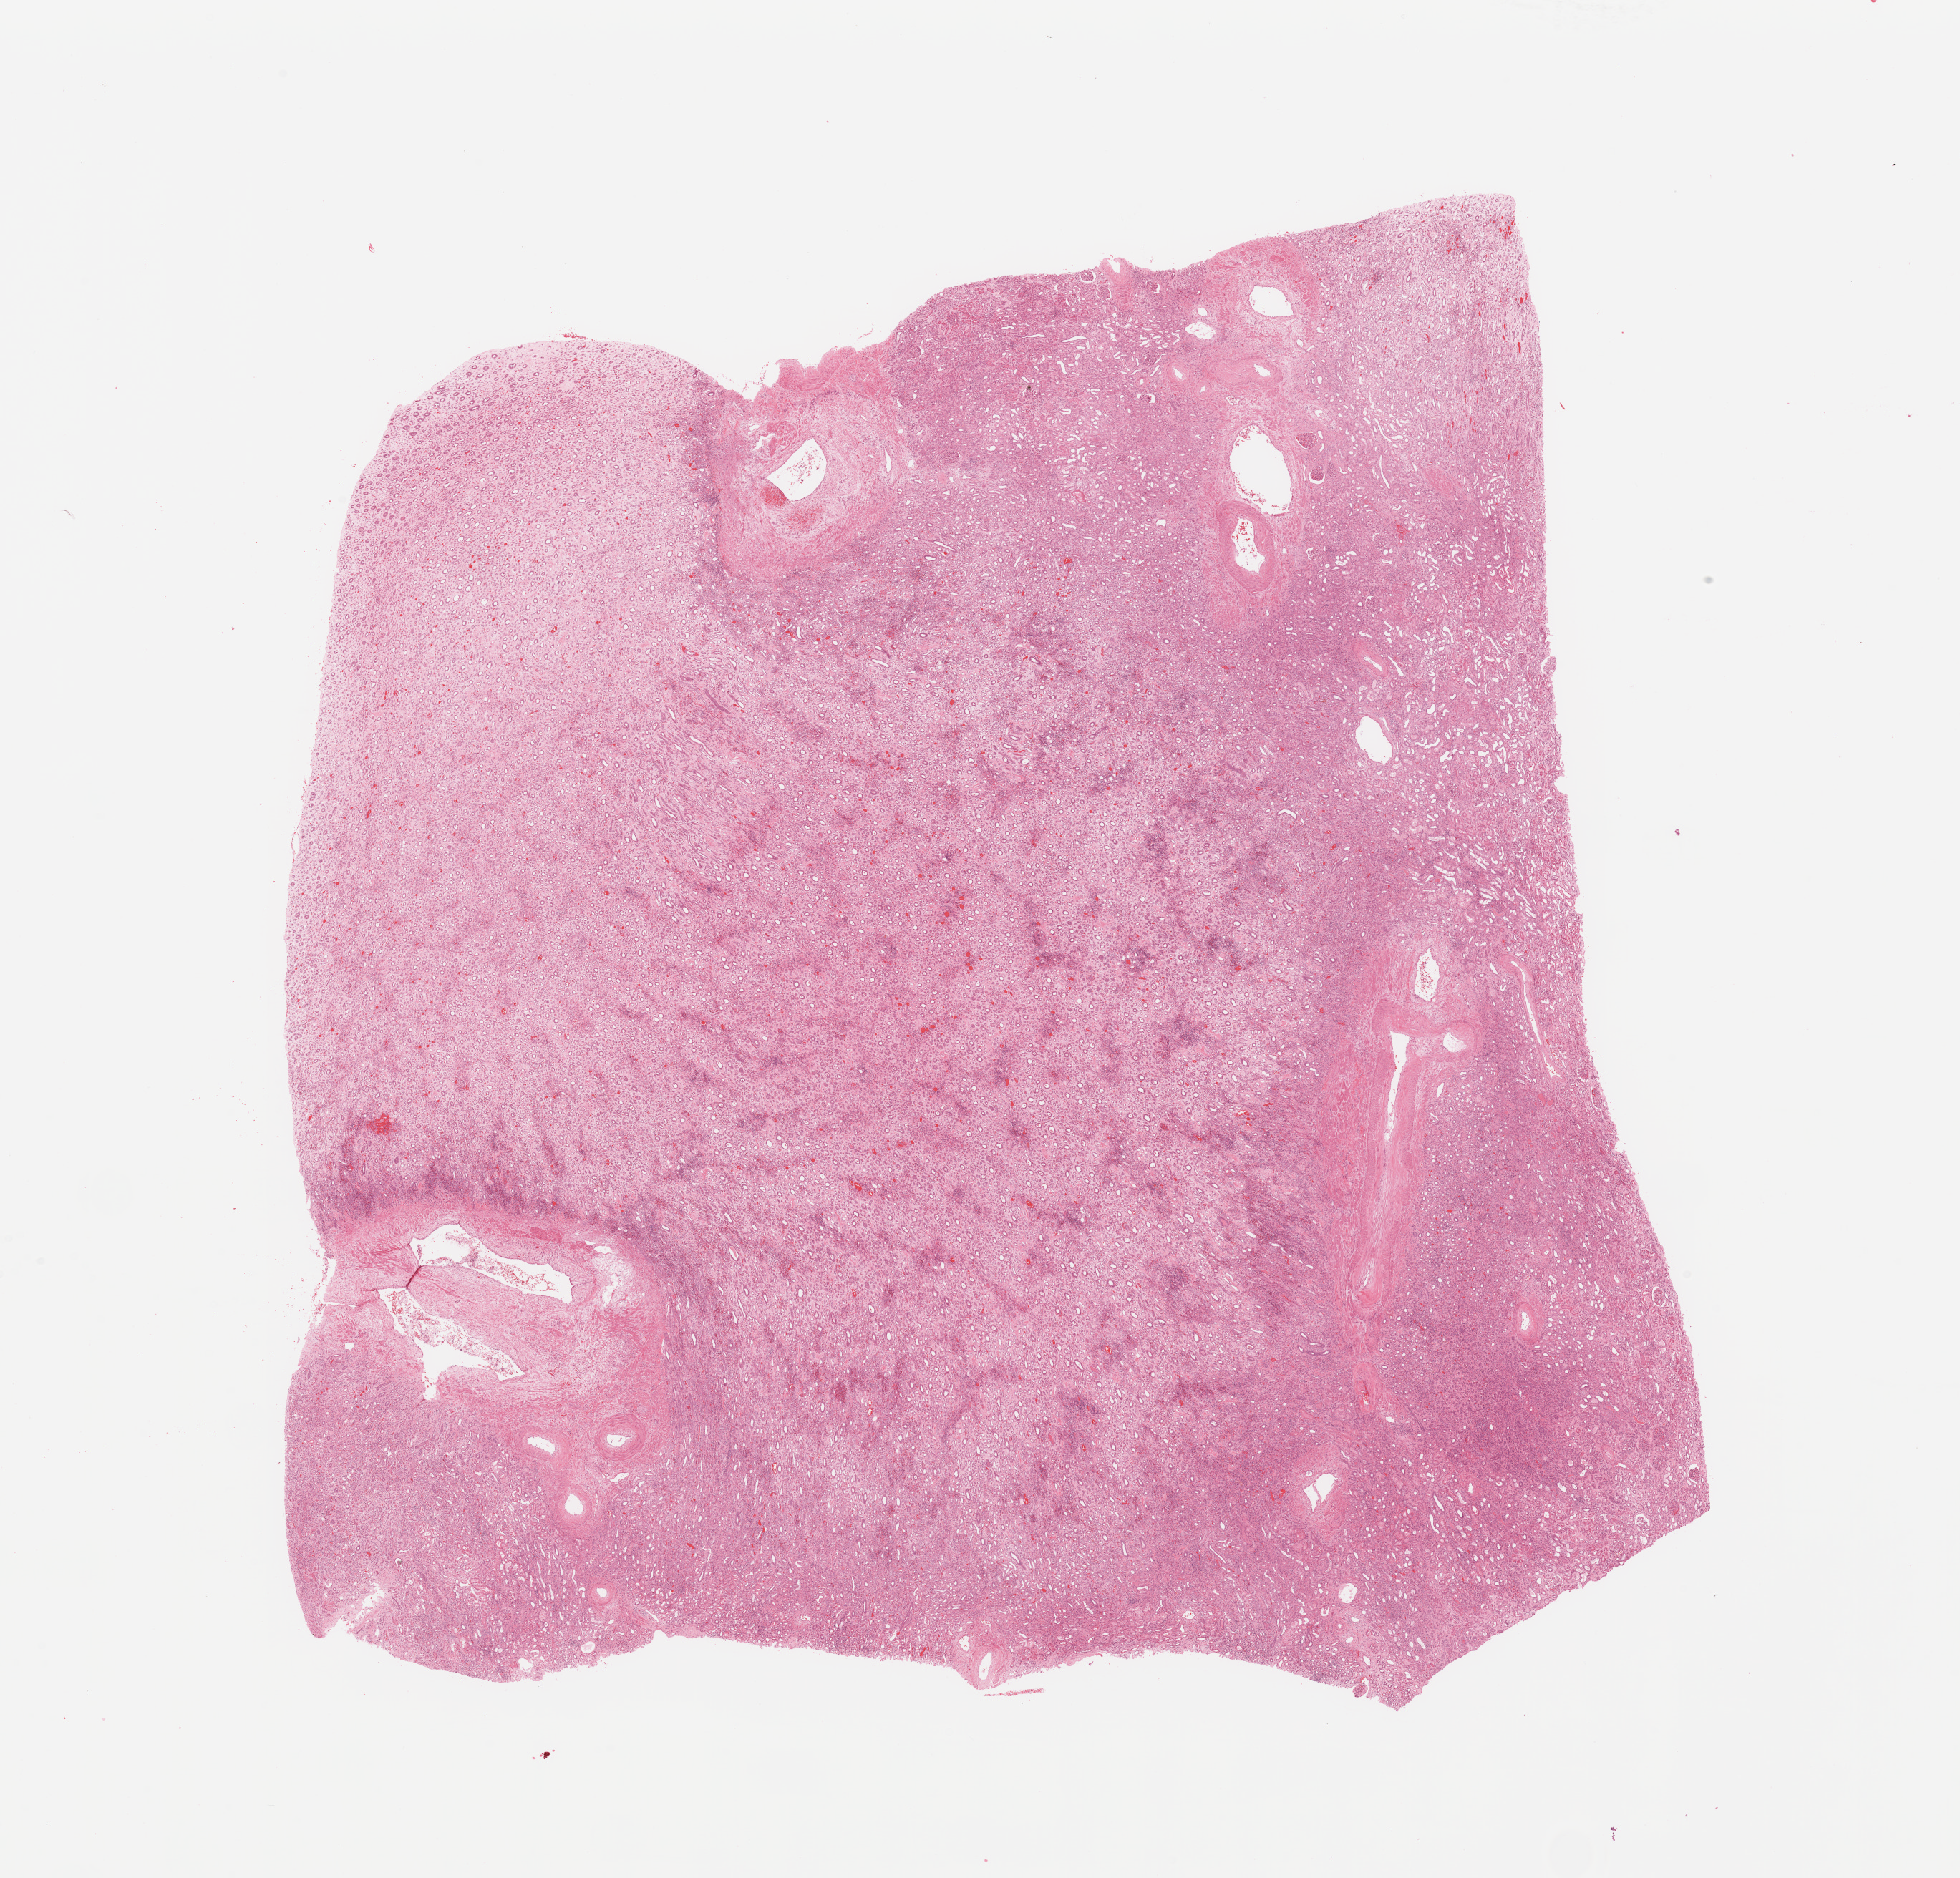
Digitized H&E-stained tissue section (whole slide), shown as a low-resolution overview of the whole scanned area (about 21.7 x 20.8 mm), kidney, normal (non-tumour) tissue. Male, 60 y/o.
This section: normal (non-tumour) tissue from the same patient. Patient diagnosis: Renal cell carcinoma, NOS.